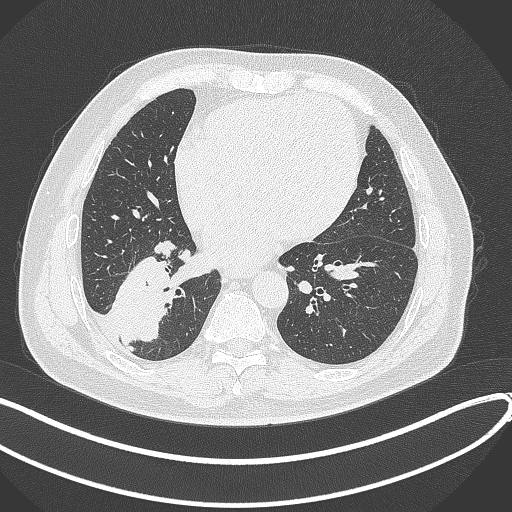
Chest CT, one axial slice. Slice 134 of 360 in the series (ordered by position). Reconstruction kernel B70f. 120 kVp. Lung window (W 1500 / L -600 HU). 512 × 512 image matrix, field of view 400 × 400 mm. Patient: male, 59 years.
Outlined on this slice (rectangle marked by the reading radiologist):
- lung tumour (recorded histology: adenocarcinoma): box from (x=108, y=249) to (x=178, y=345) px